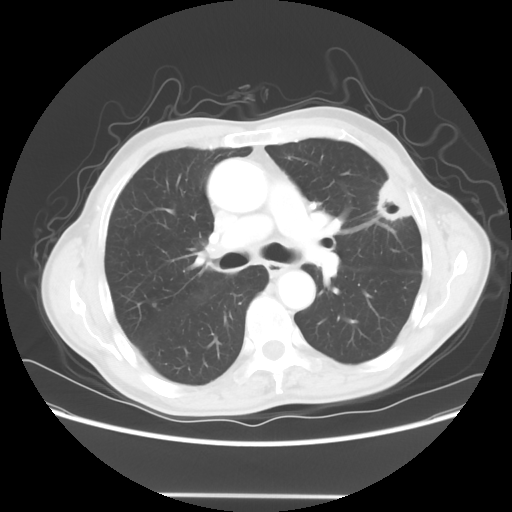
Chest CT, one axial slice; slice 38 of 64 in the series (ordered by position); reconstruction kernel STANDARD; lung window (W 1500 / L -600 HU); 512 × 512 image matrix, field of view 392 × 392 mm. Patient: male, 71 years. From the clinical record (not read from this slice): clinical TNM (as recorded): T1c N0 M0.
Structures marked on this image (rectangle marked by the reading radiologist):
- lung tumour (recorded histology: adenocarcinoma): bounding box [x1, y1, x2, y2] px = [364, 171, 419, 235]